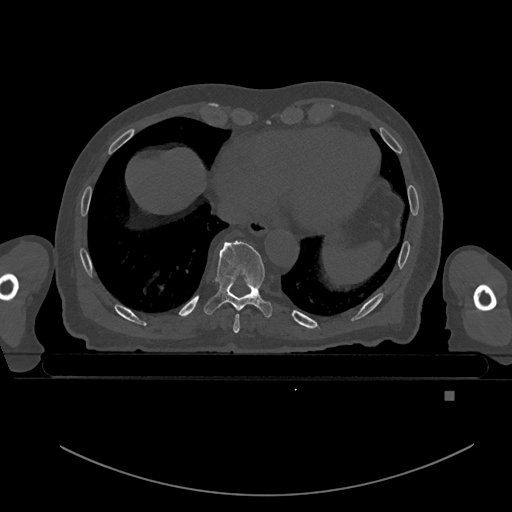
CT including the spine, one axial slice. Slice 151 of 969 in the series (ordered by position). Bone window (W 1800 / L 400 HU). 512 × 512 image matrix. Patient: male, 82 years. From the clinical record (not read from this slice): primary cancer: prostate; vertebrae with lytic lesions (as recorded): T11, T9, T8, T2.
Structures marked on this image (semi-automatic segmentation, software-assisted and operator-edited):
- T8 vertebra: box from (x=233, y=314) to (x=240, y=333) px
- T9 vertebra: (x=204, y=241)–(x=272, y=318)